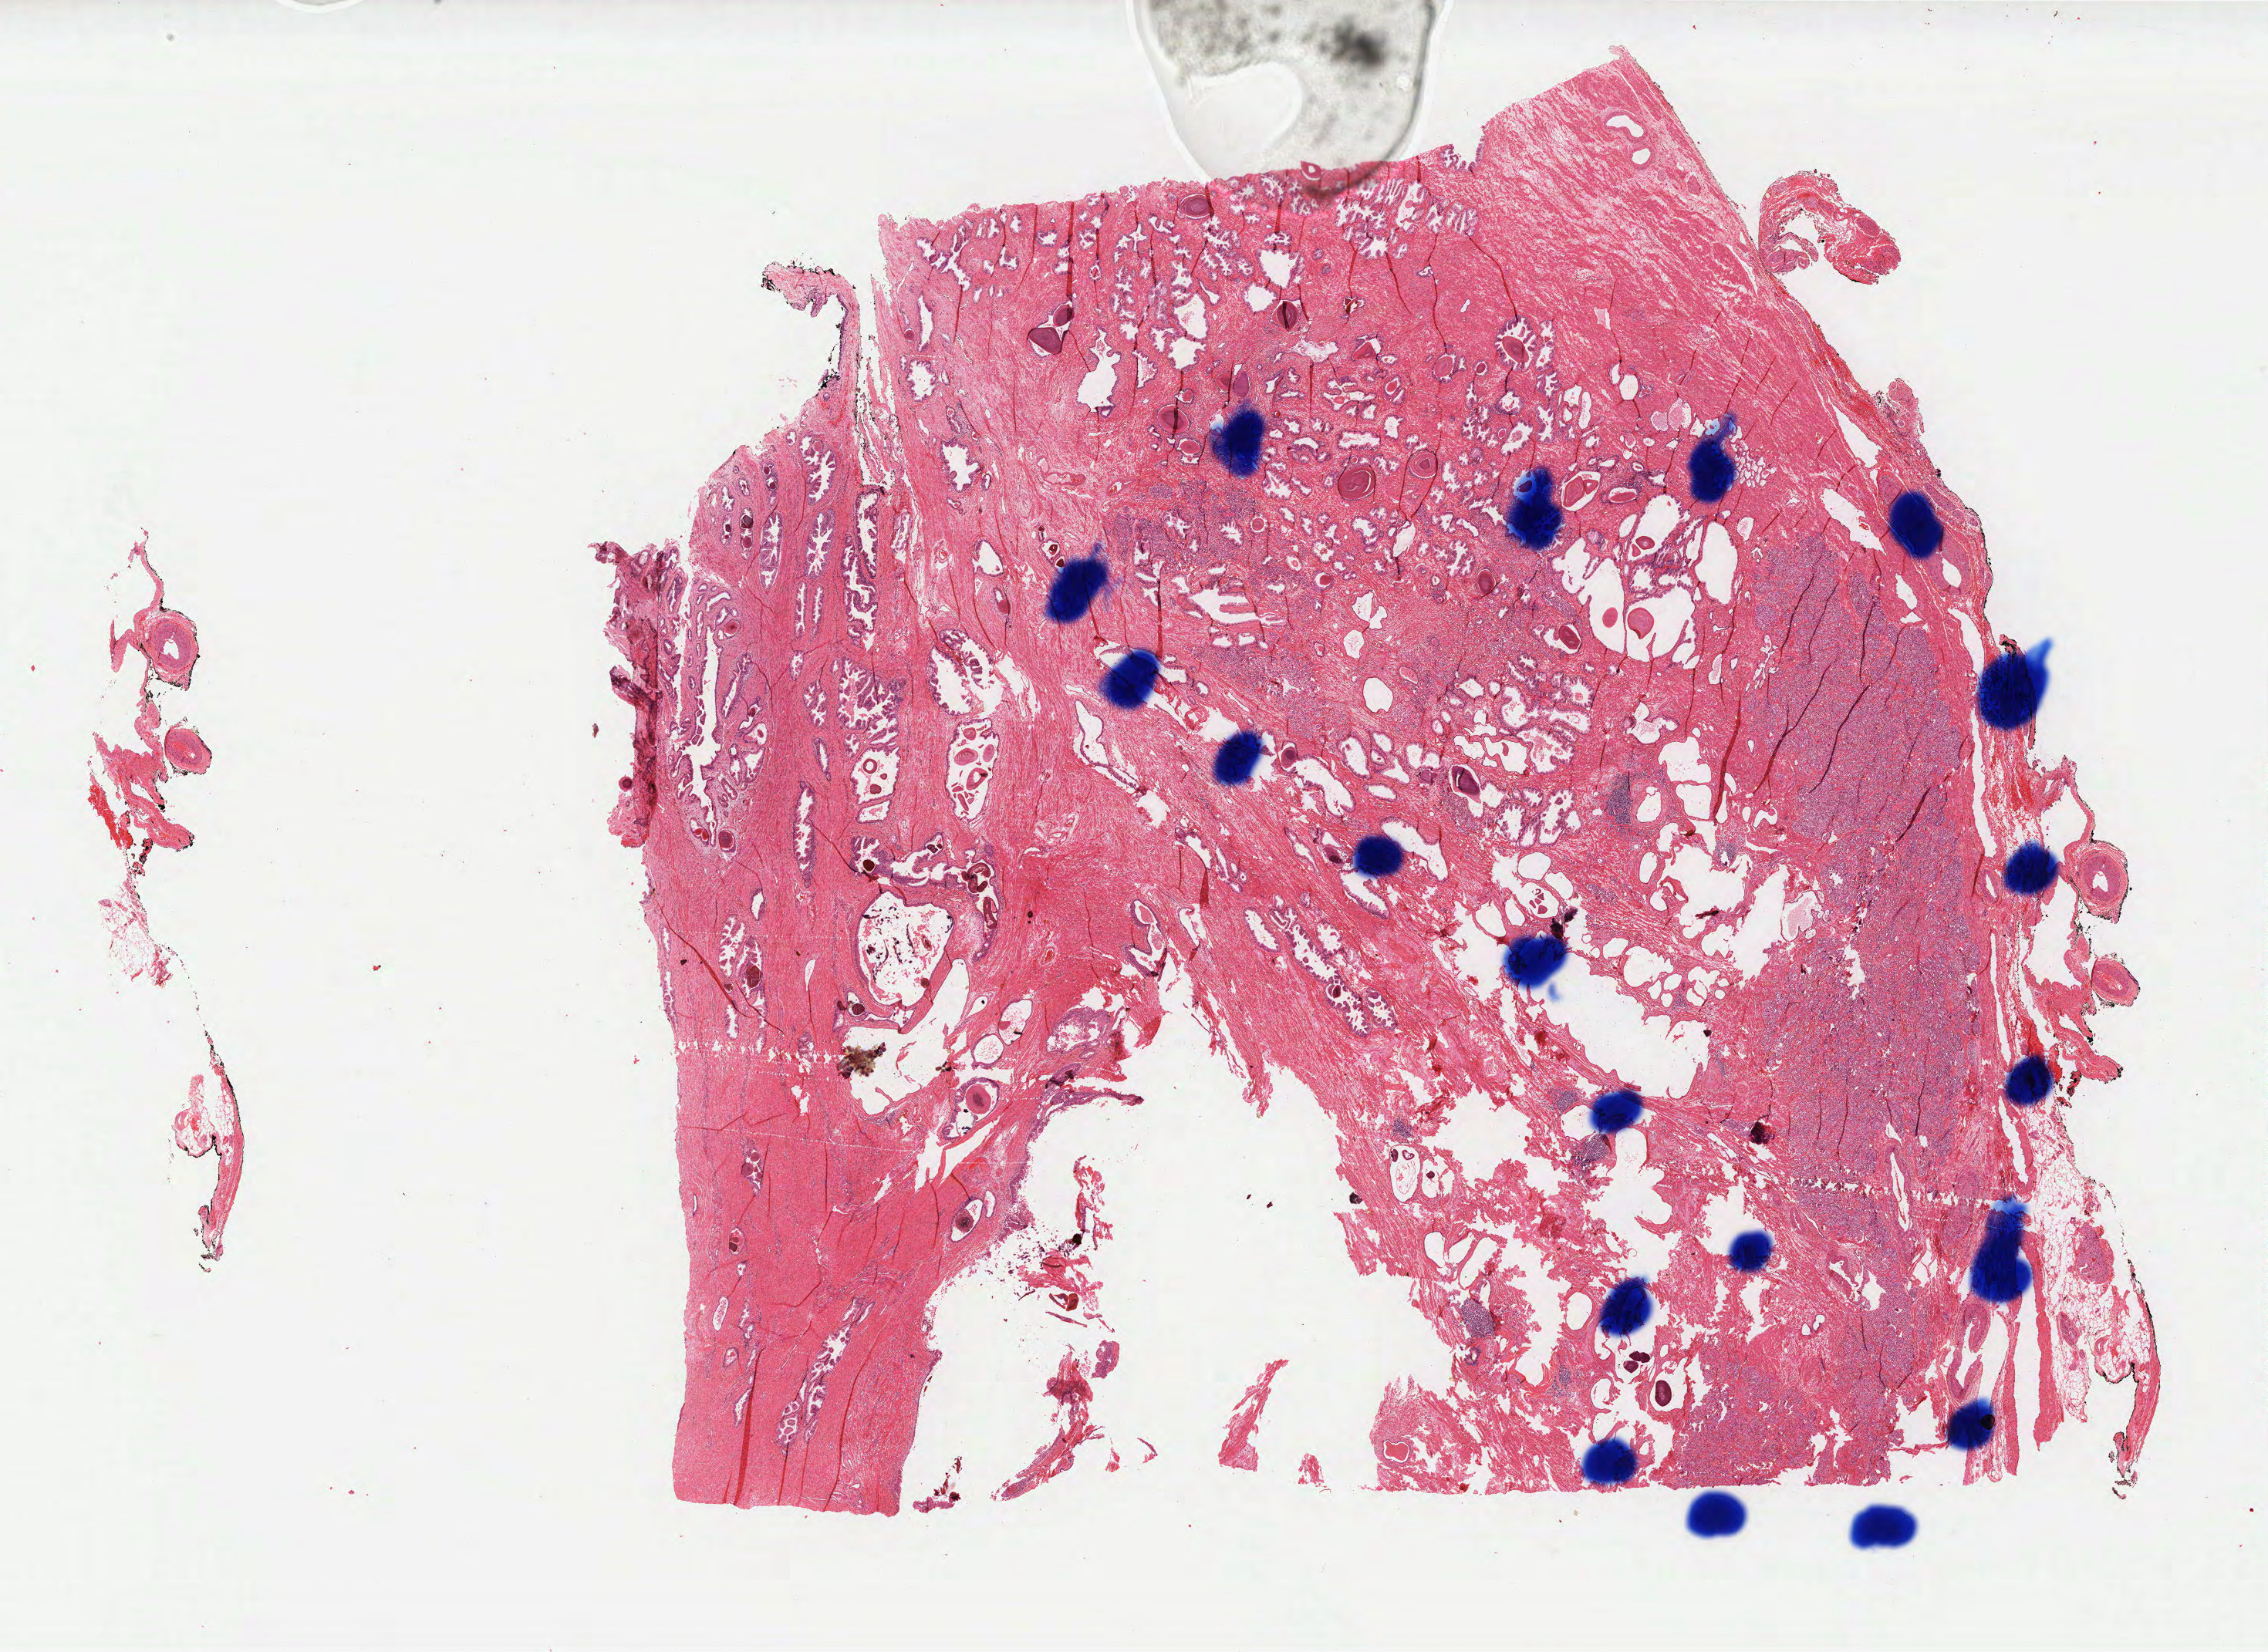
Whole-slide histology image, H&E-stained, a low-resolution overview of the entire scanned area, about 23.5 x 17.1 mm; formalin-fixed paraffin-embedded (FFPE) diagnostic section; sample: primary tumour, prostate. Patient: male, age at initial diagnosis 70 years. Gleason score: 9 (4+5).
• histologic diagnosis: Adenocarcinoma, NOS (prostate gland)
• lymph nodes positive (case pathology): 0 of 2 examined